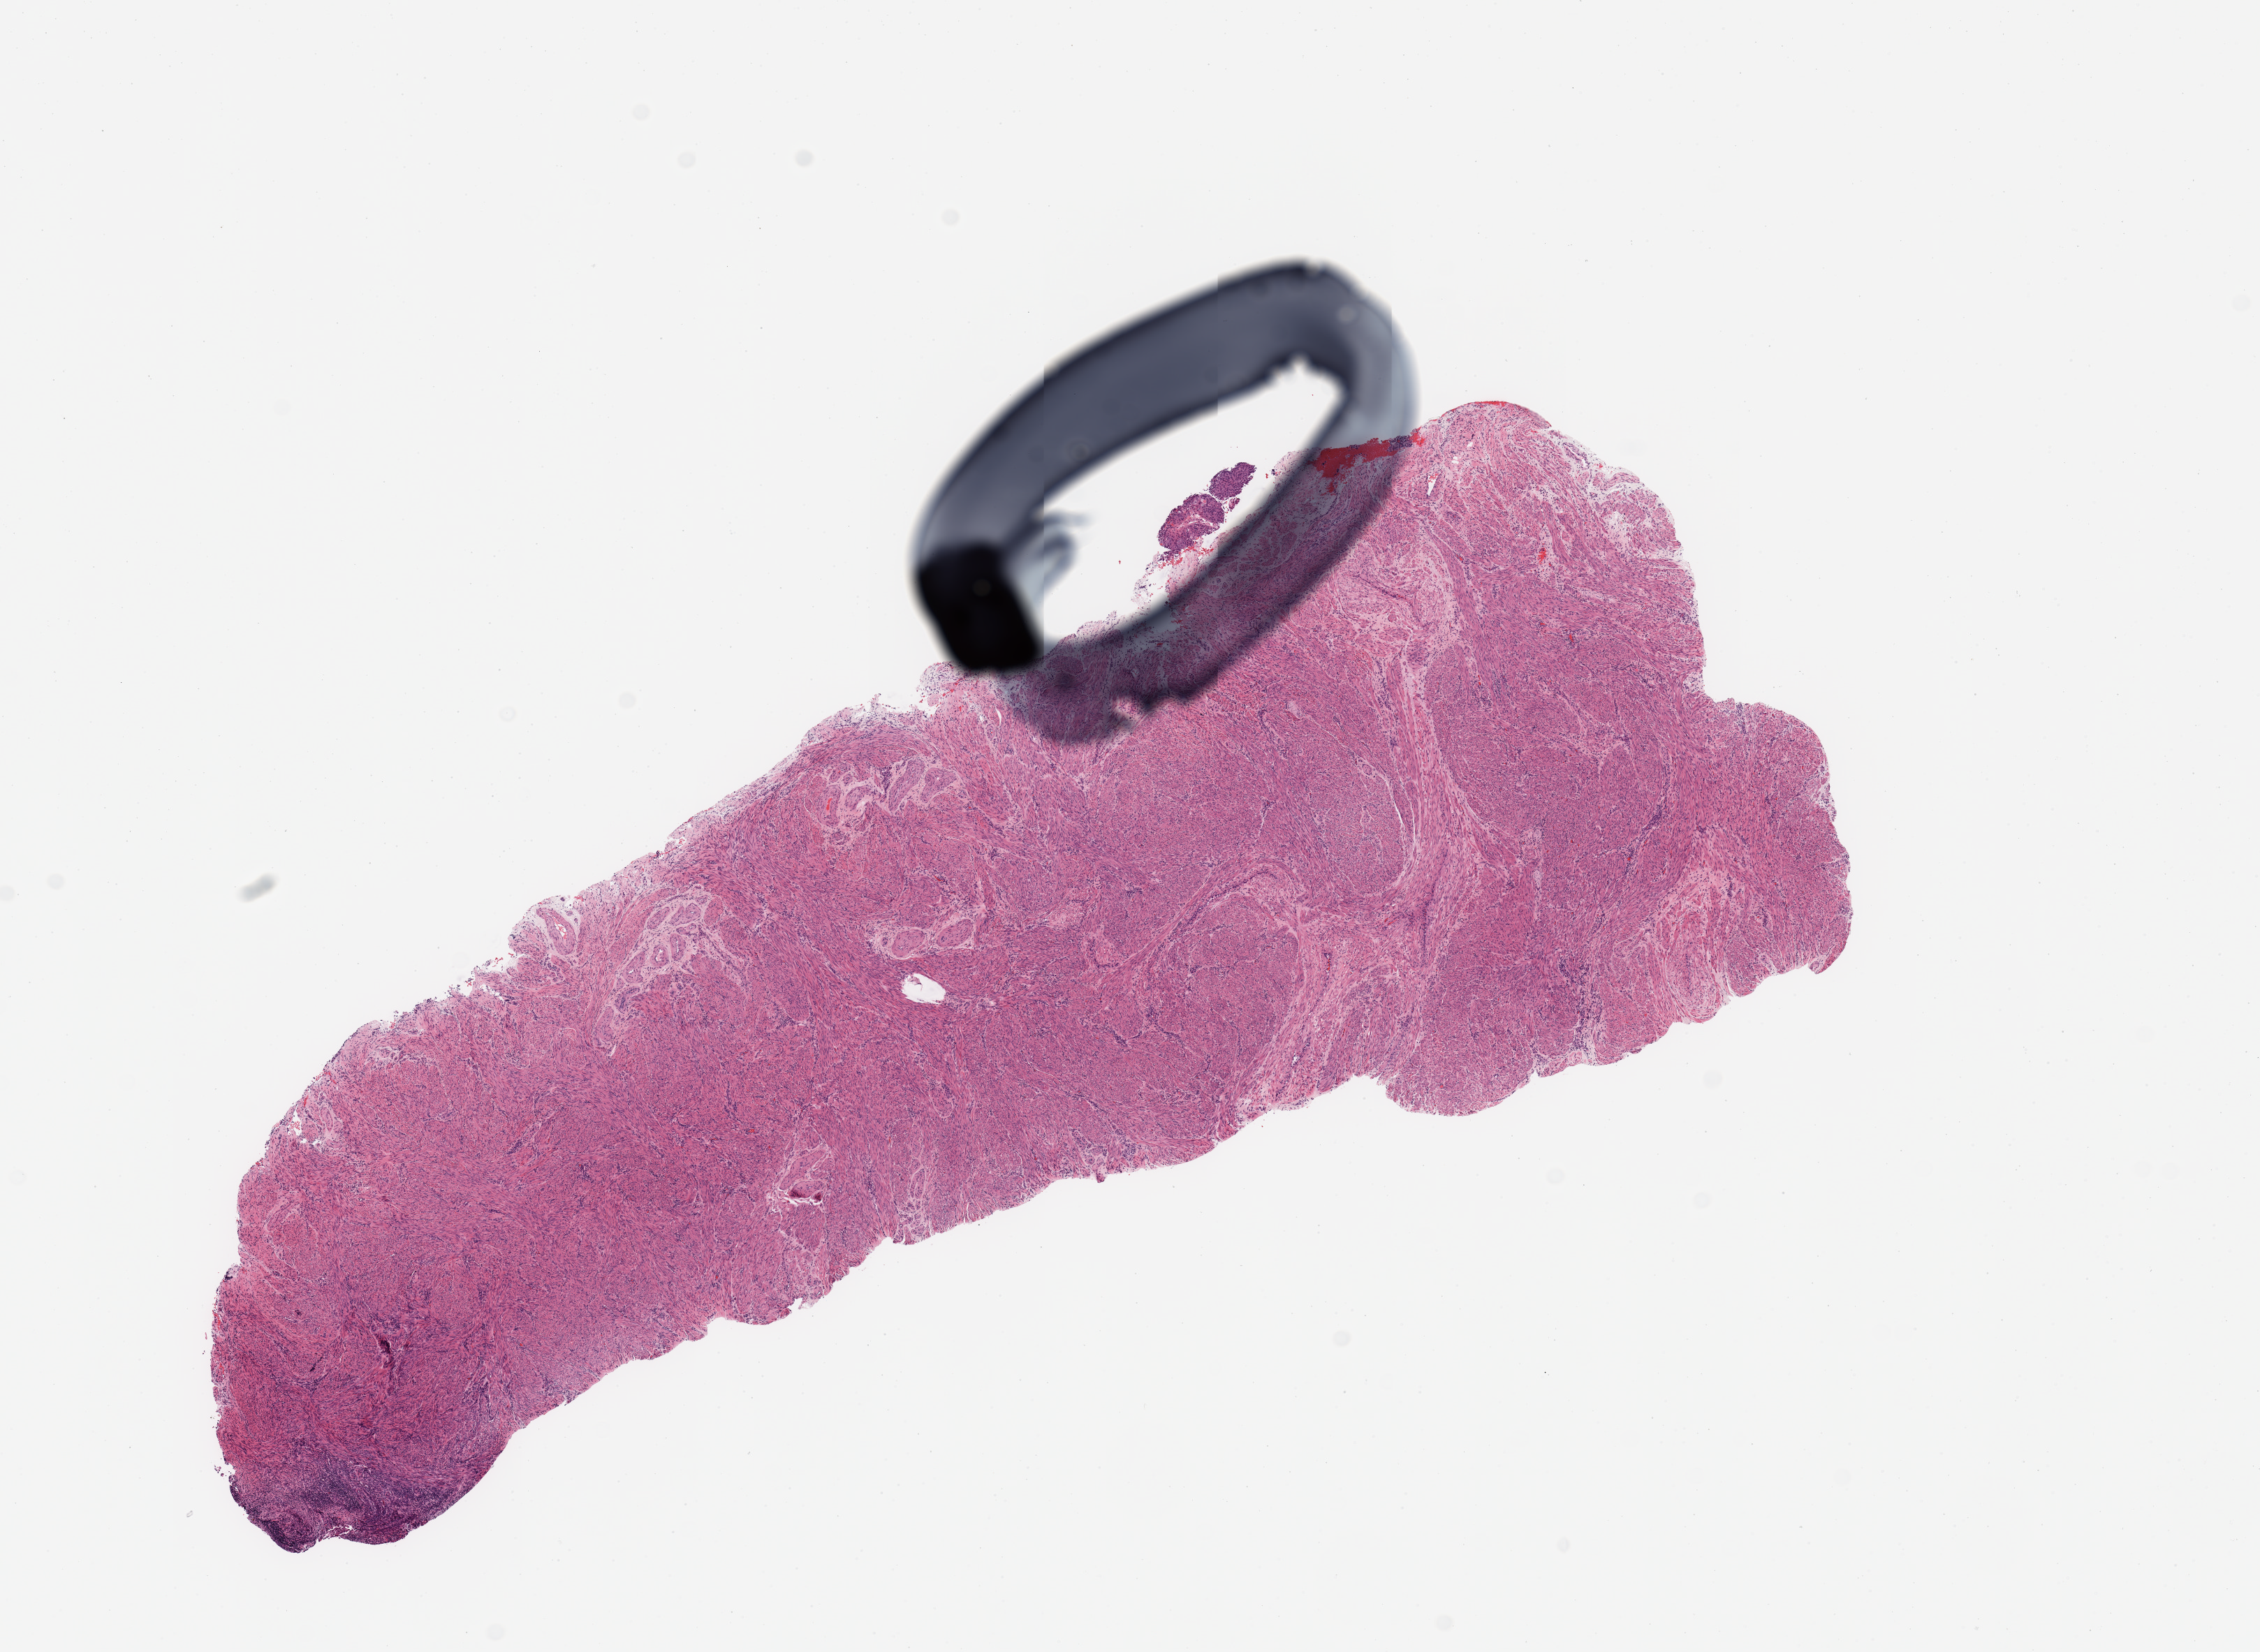
Whole-slide histology image, H&E-stained, low-resolution overview of the scanned area, about 12.8 x 9.4 mm (slide scanned at 20x); normal (non-tumour) tissue sample, uterus. Female, 50 y/o.
* this section: normal (non-tumour) tissue from the same patient
* patient diagnosis: Endometrioid adenocarcinoma, NOS